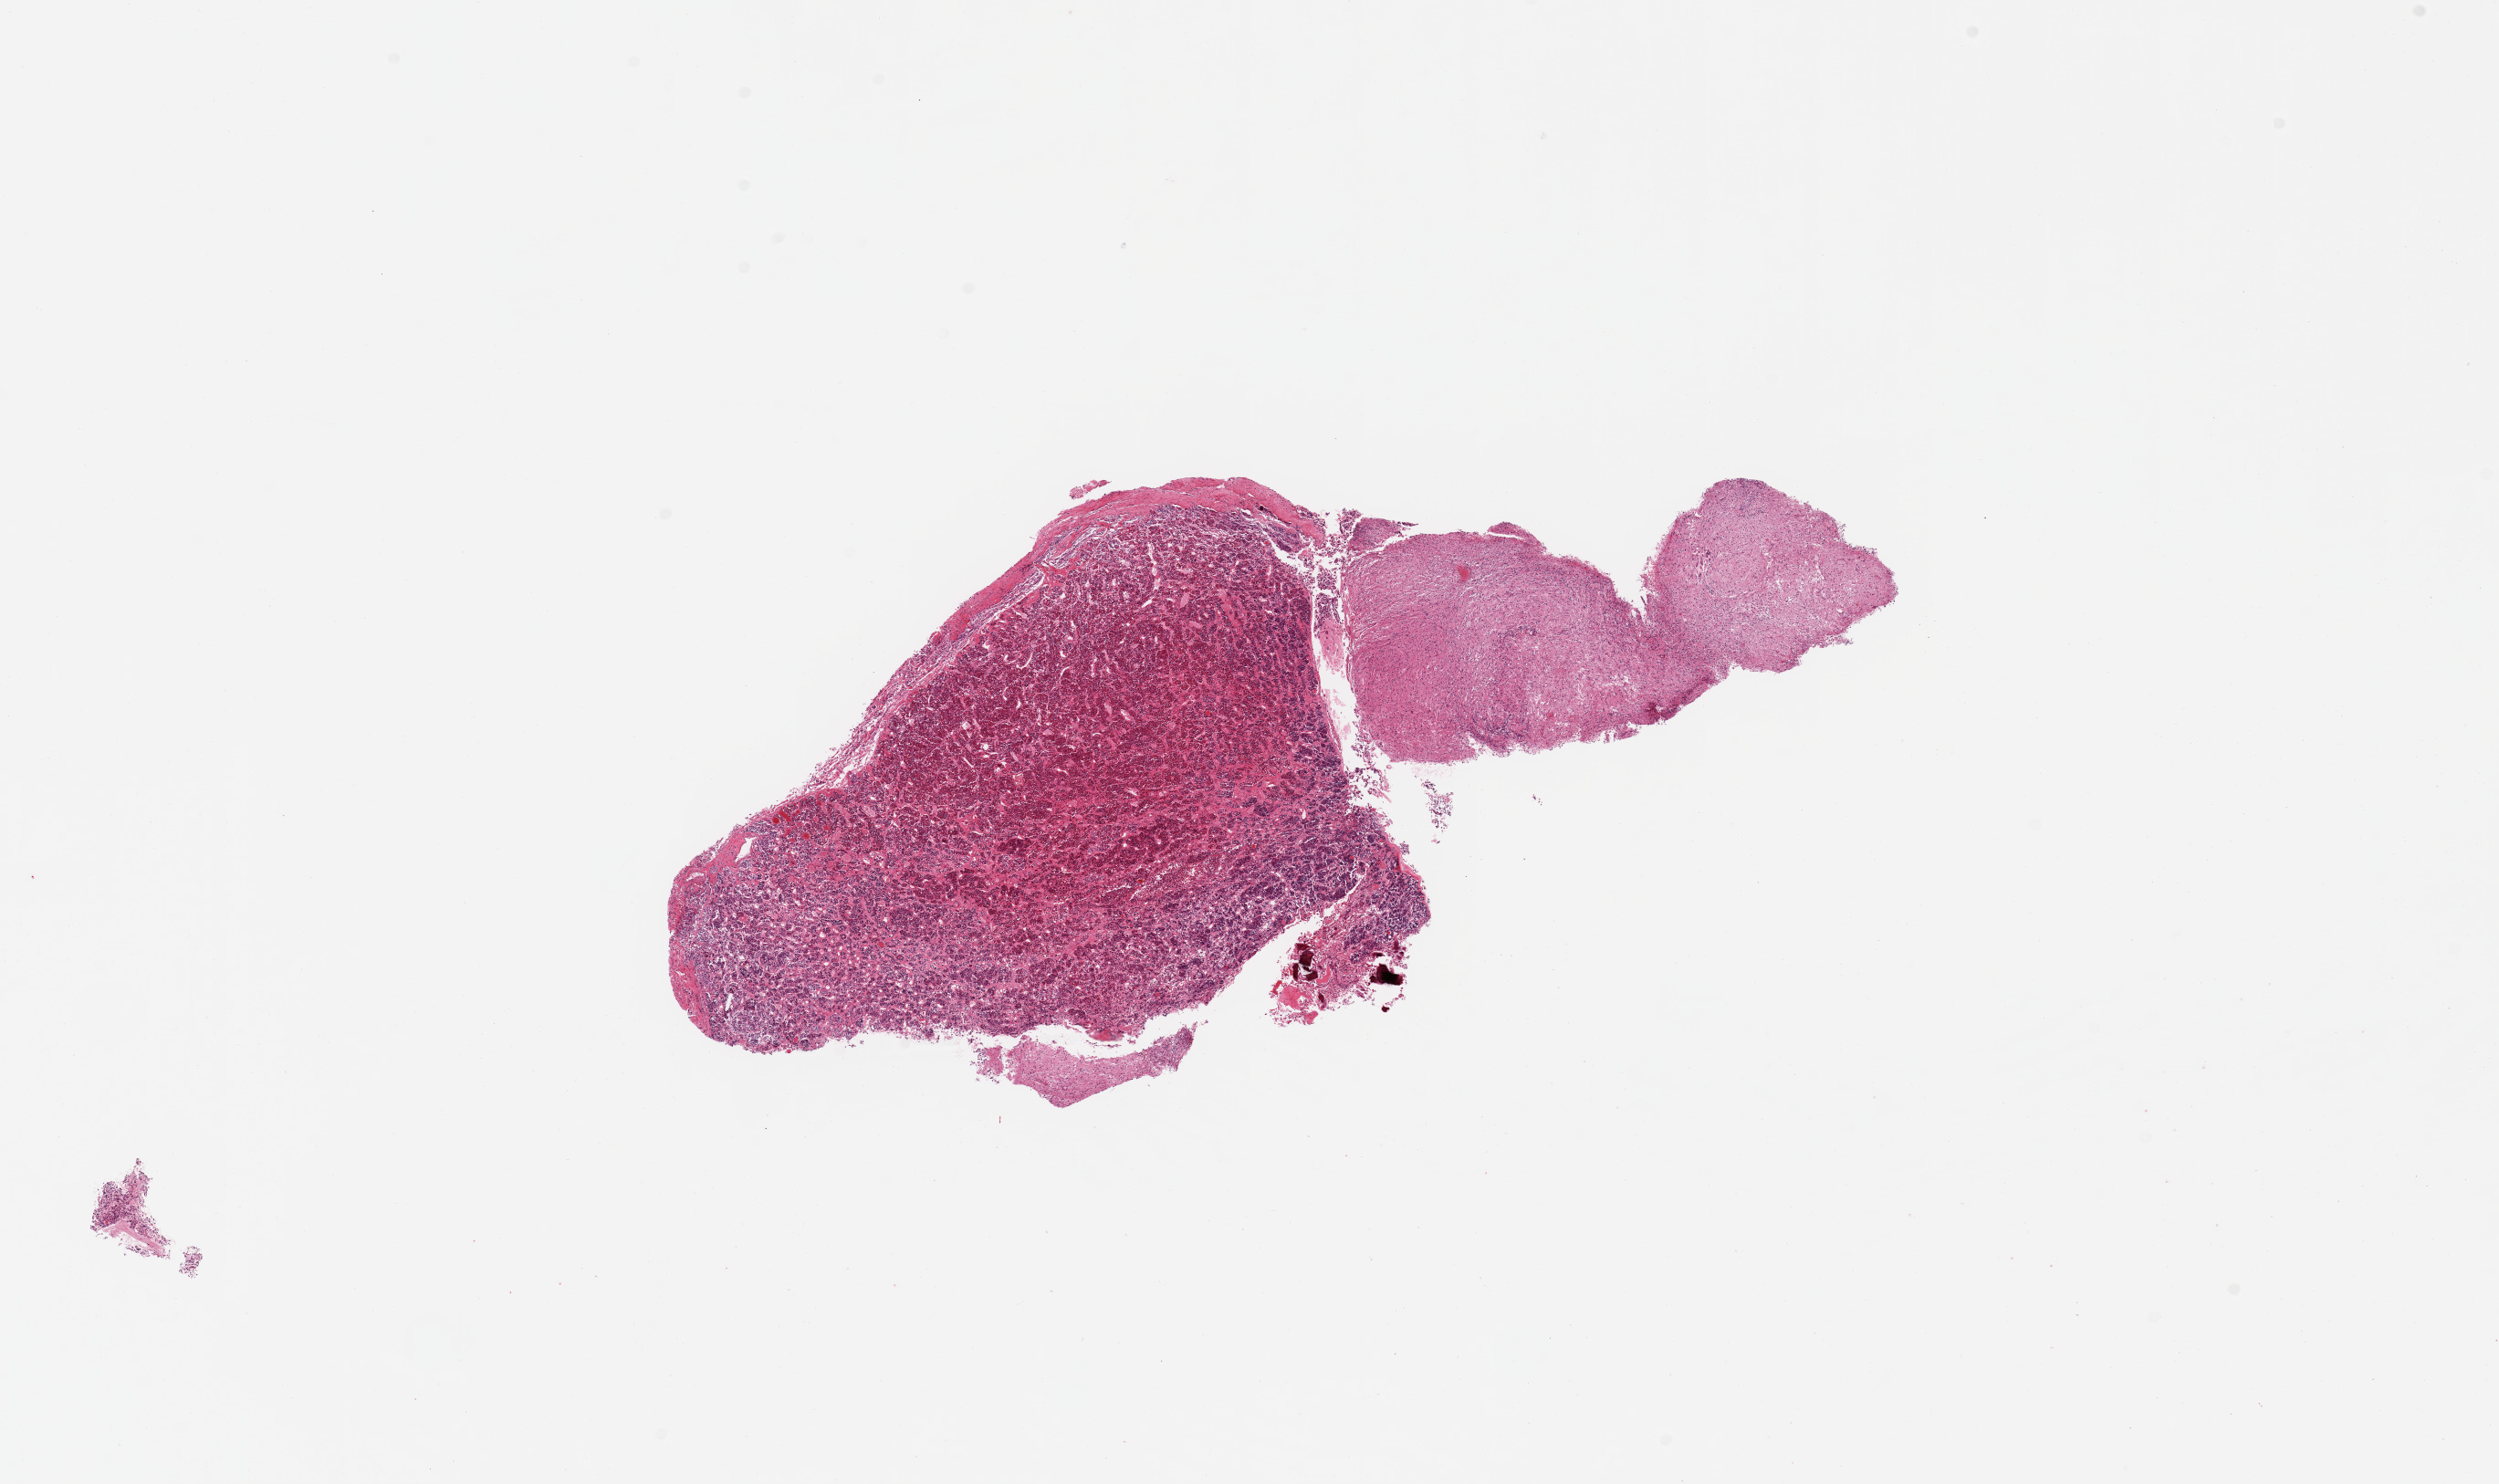
Whole-slide image, haematoxylin and eosin stain, shown as a low-resolution overview of the whole scanned area (about 21.7 x 12.9 mm). PAXgene-fixed, paraffin-embedded tissue. Section of pituitary (target tissue). Tissue donor sample. Male donor.
Review note (as recorded): 1 piece; posterior and anterior lobes present.